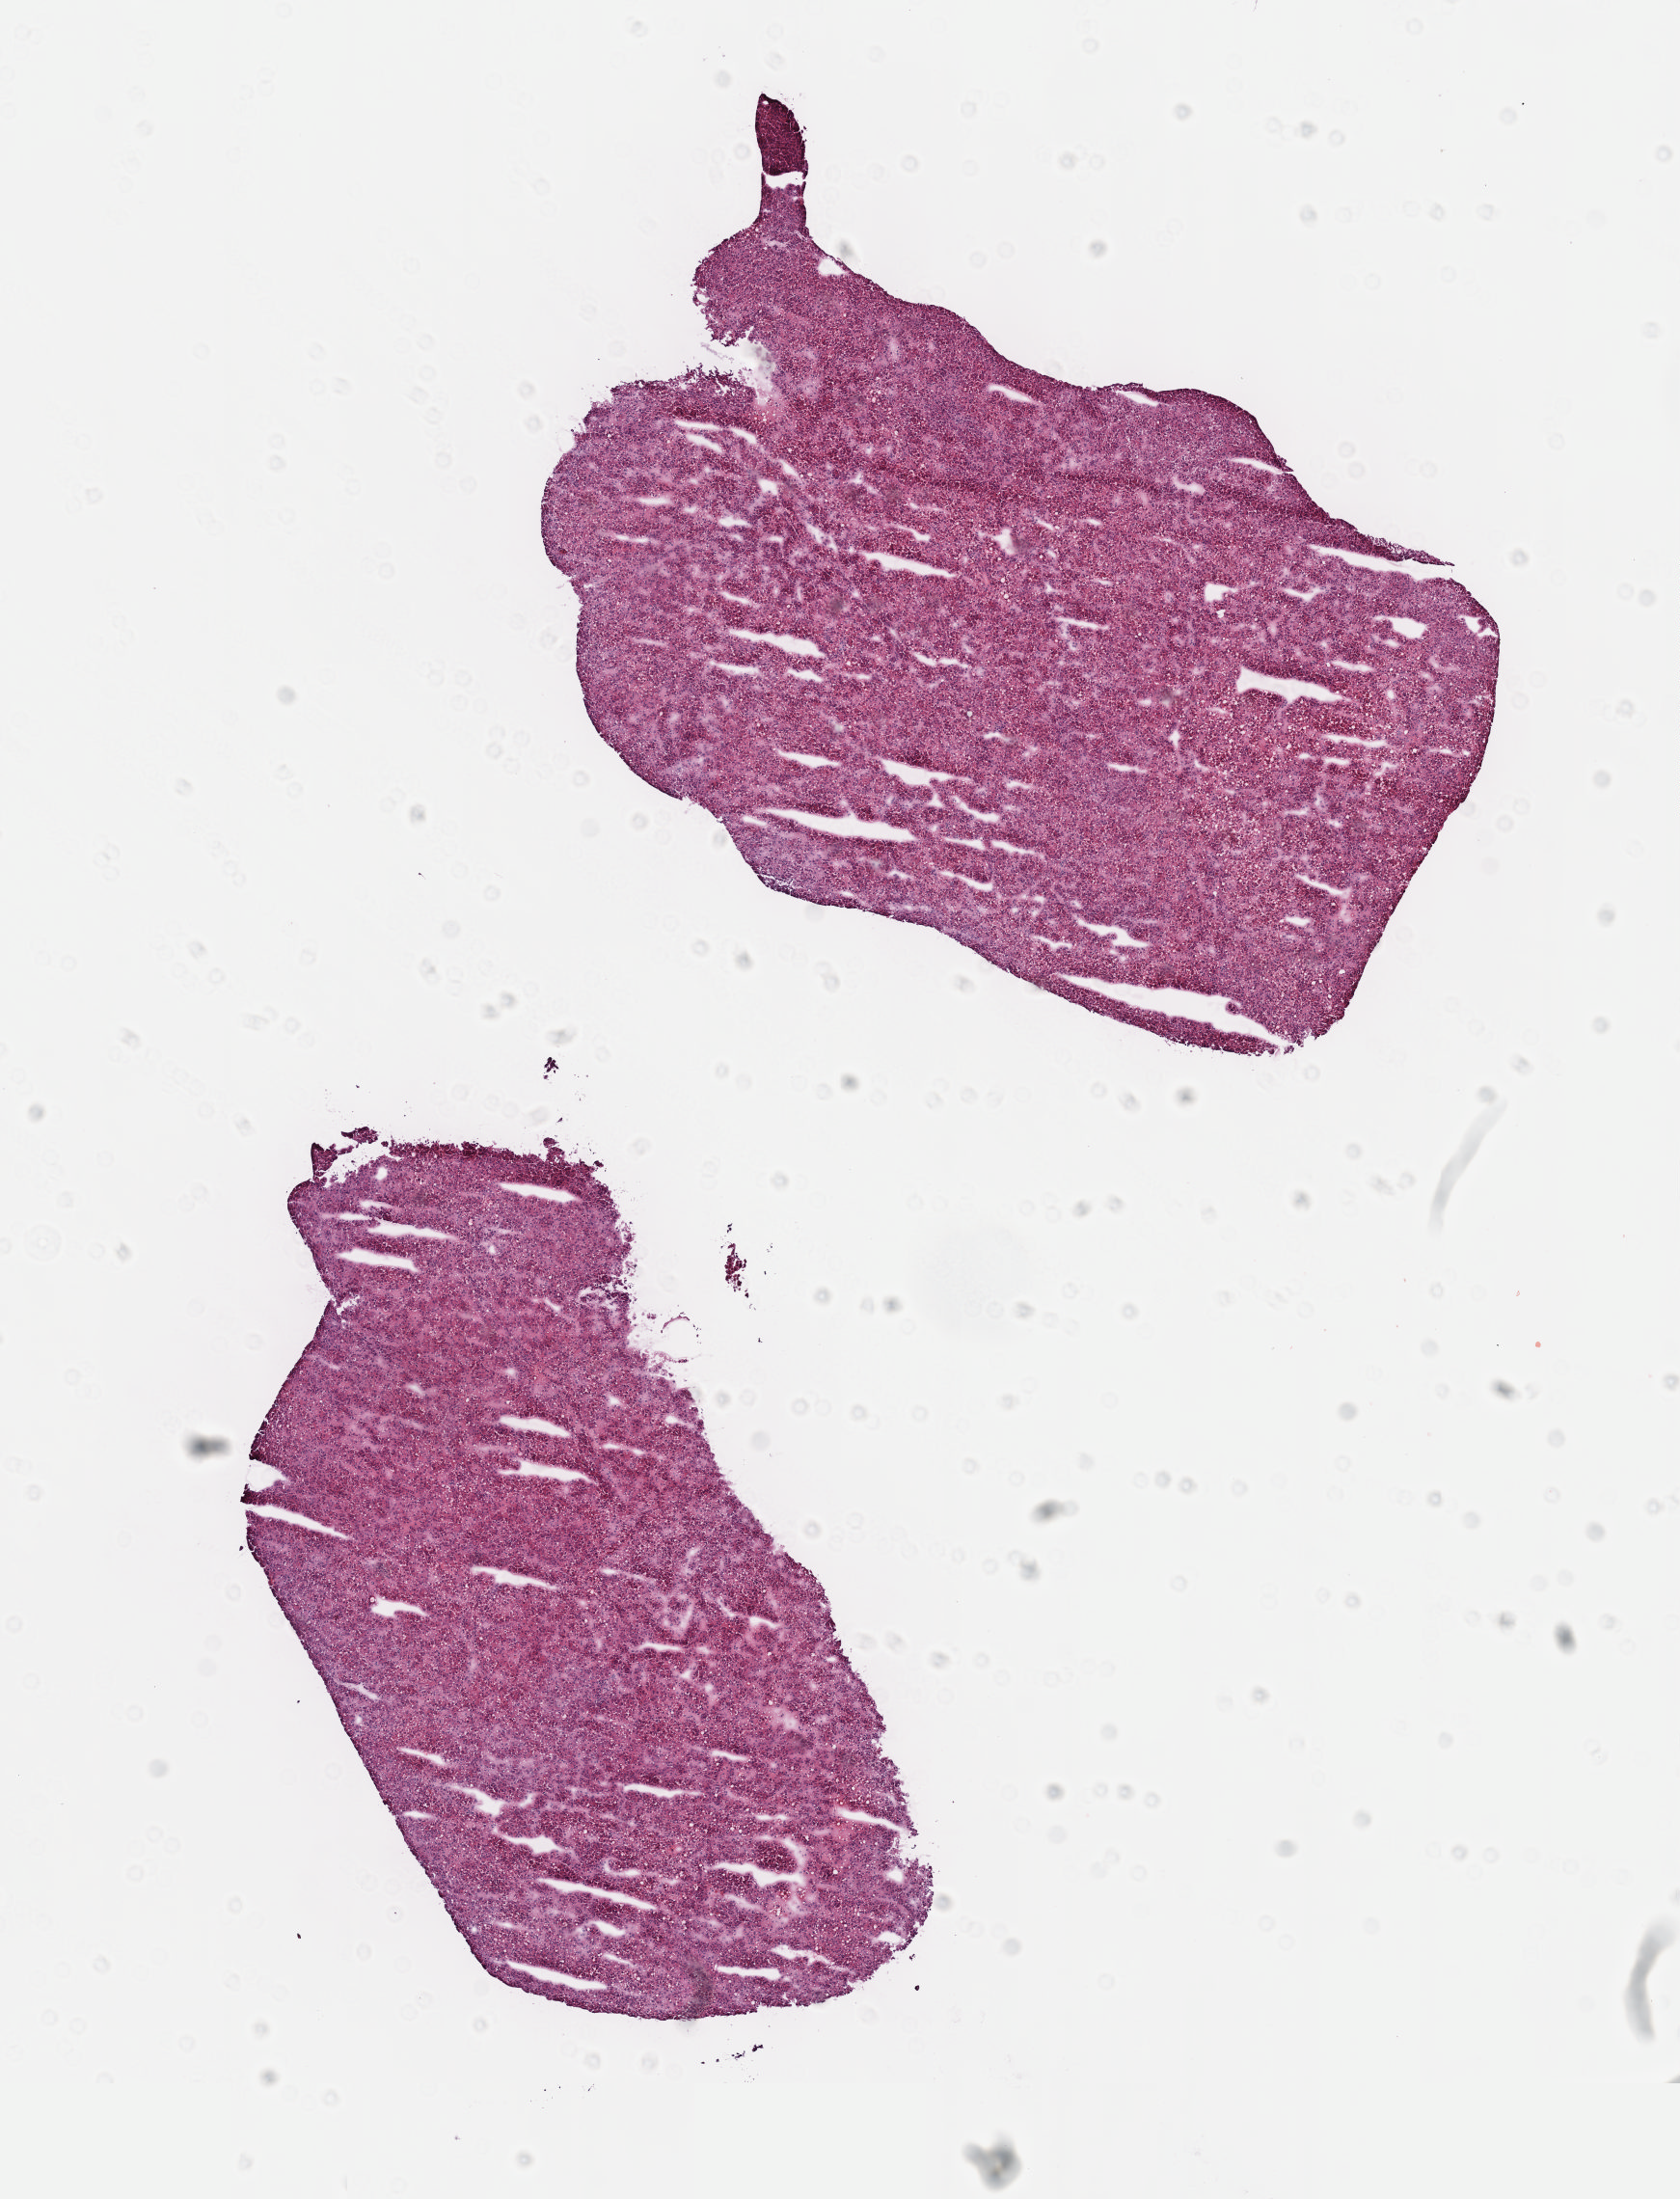
Whole-slide histology image, H&E-stained — low-resolution overview of the scanned area, about 7.0 x 9.2 mm (acquisition: 40x scan). Frozen section. Liver, primary tumour sample. Female patient; age at initial diagnosis 70 years. Histologic grade: G3 (poorly differentiated). Composition of this section per pathologist review: tumour cells 90%, tumour nuclei 95%, normal cells 0%, stromal cells 10%, necrosis 0%. Infiltration values recorded for this section: lymphocyte infiltration 0%, monocyte infiltration 0%, neutrophil infiltration 0%.
Diagnosis: Hepatocellular carcinoma, NOS. AJCC pathologic stage: I.